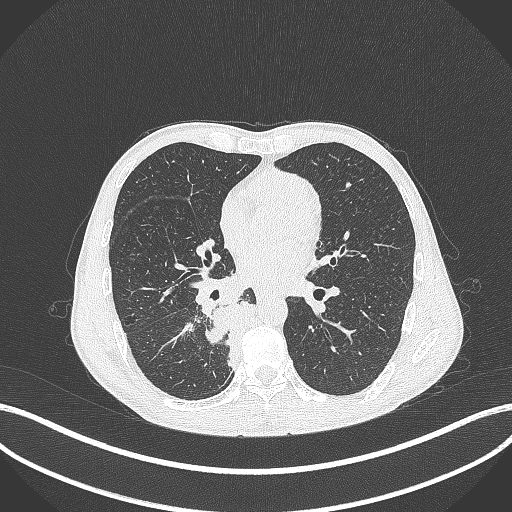
Chest CT, one axial slice; position 181 of 371 along the scan axis; reconstruction kernel B70f; 120 kVp; lung window (W 1500 / L -600 HU); 1 mm slice thickness; 512 × 512 image matrix. Patient: male, 58 years. From the clinical record (not read from this slice): clinical TNM (as recorded): T3 N1 M1.
Structures marked on this image (rectangle marked by the reading radiologist):
- lung tumour (recorded histology: squamous cell carcinoma): bounding box [x1, y1, x2, y2] px = [200, 301, 263, 368]